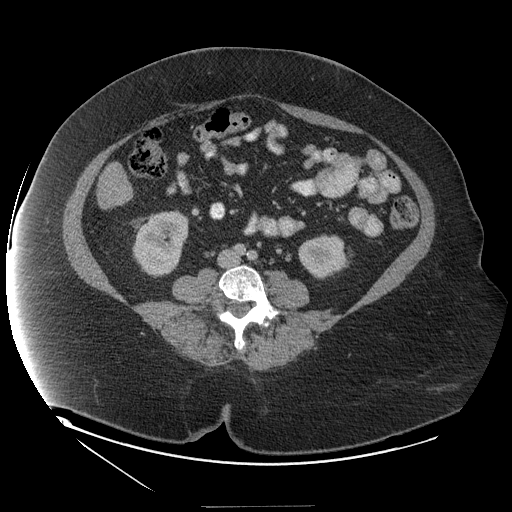
Contrast-enhanced abdominal CT (liver protocol), one axial slice; position 22 of 127 along the scan axis; 140 kVp; soft-tissue window (W 400 / L 40 HU); 2.5 mm slice thickness; 512 × 512 image matrix, field of view 480 × 480 mm. From the clinical record (not read from this slice): diagnosis: hepatocellular carcinoma (patient treated with transarterial chemoembolisation; whether this scan precedes or follows treatment is not stated here); TNM stage (as recorded): Stage-II; Child-Pugh class: A.
Outlined on this slice (semi-automatically segmented with operator editing):
- liver parenchyma outside the tumour (the mass and vessels are separate outlines, so this box may not span the whole liver): bounding box [x1, y1, x2, y2] px = [96, 162, 132, 208]